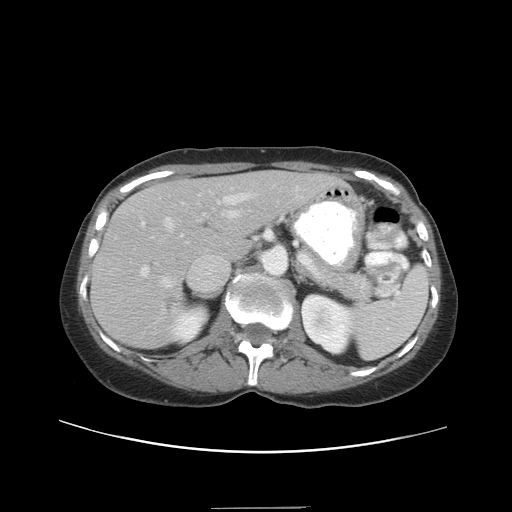
Contrast-enhanced abdominal CT, one axial slice. Position 24 of 38 along the scan axis. Reconstruction kernel STANDARD. Intravenous contrast given. Soft-tissue window (W 400 / L 40 HU). 5 mm slice thickness. 512 × 512 image matrix. Female patient, age 64 years. Case-level facts recorded for this patient, not image findings: diagnosis: colorectal cancer liver metastases, imaged before liver resection; multiple liver metastases: no; largest metastasis: 3.8 cm; disease in both lobes: yes.
Structures marked on this image (manually delineated by an expert):
- hepatic veins: bounding box [x1, y1, x2, y2] px = [160, 194, 251, 288]
- liver: [93, 171, 333, 347]
- planned liver remnant (the part of the liver to remain after resection): [136, 172, 333, 258]
- portal vein (with intrahepatic branches): [141, 194, 250, 276]